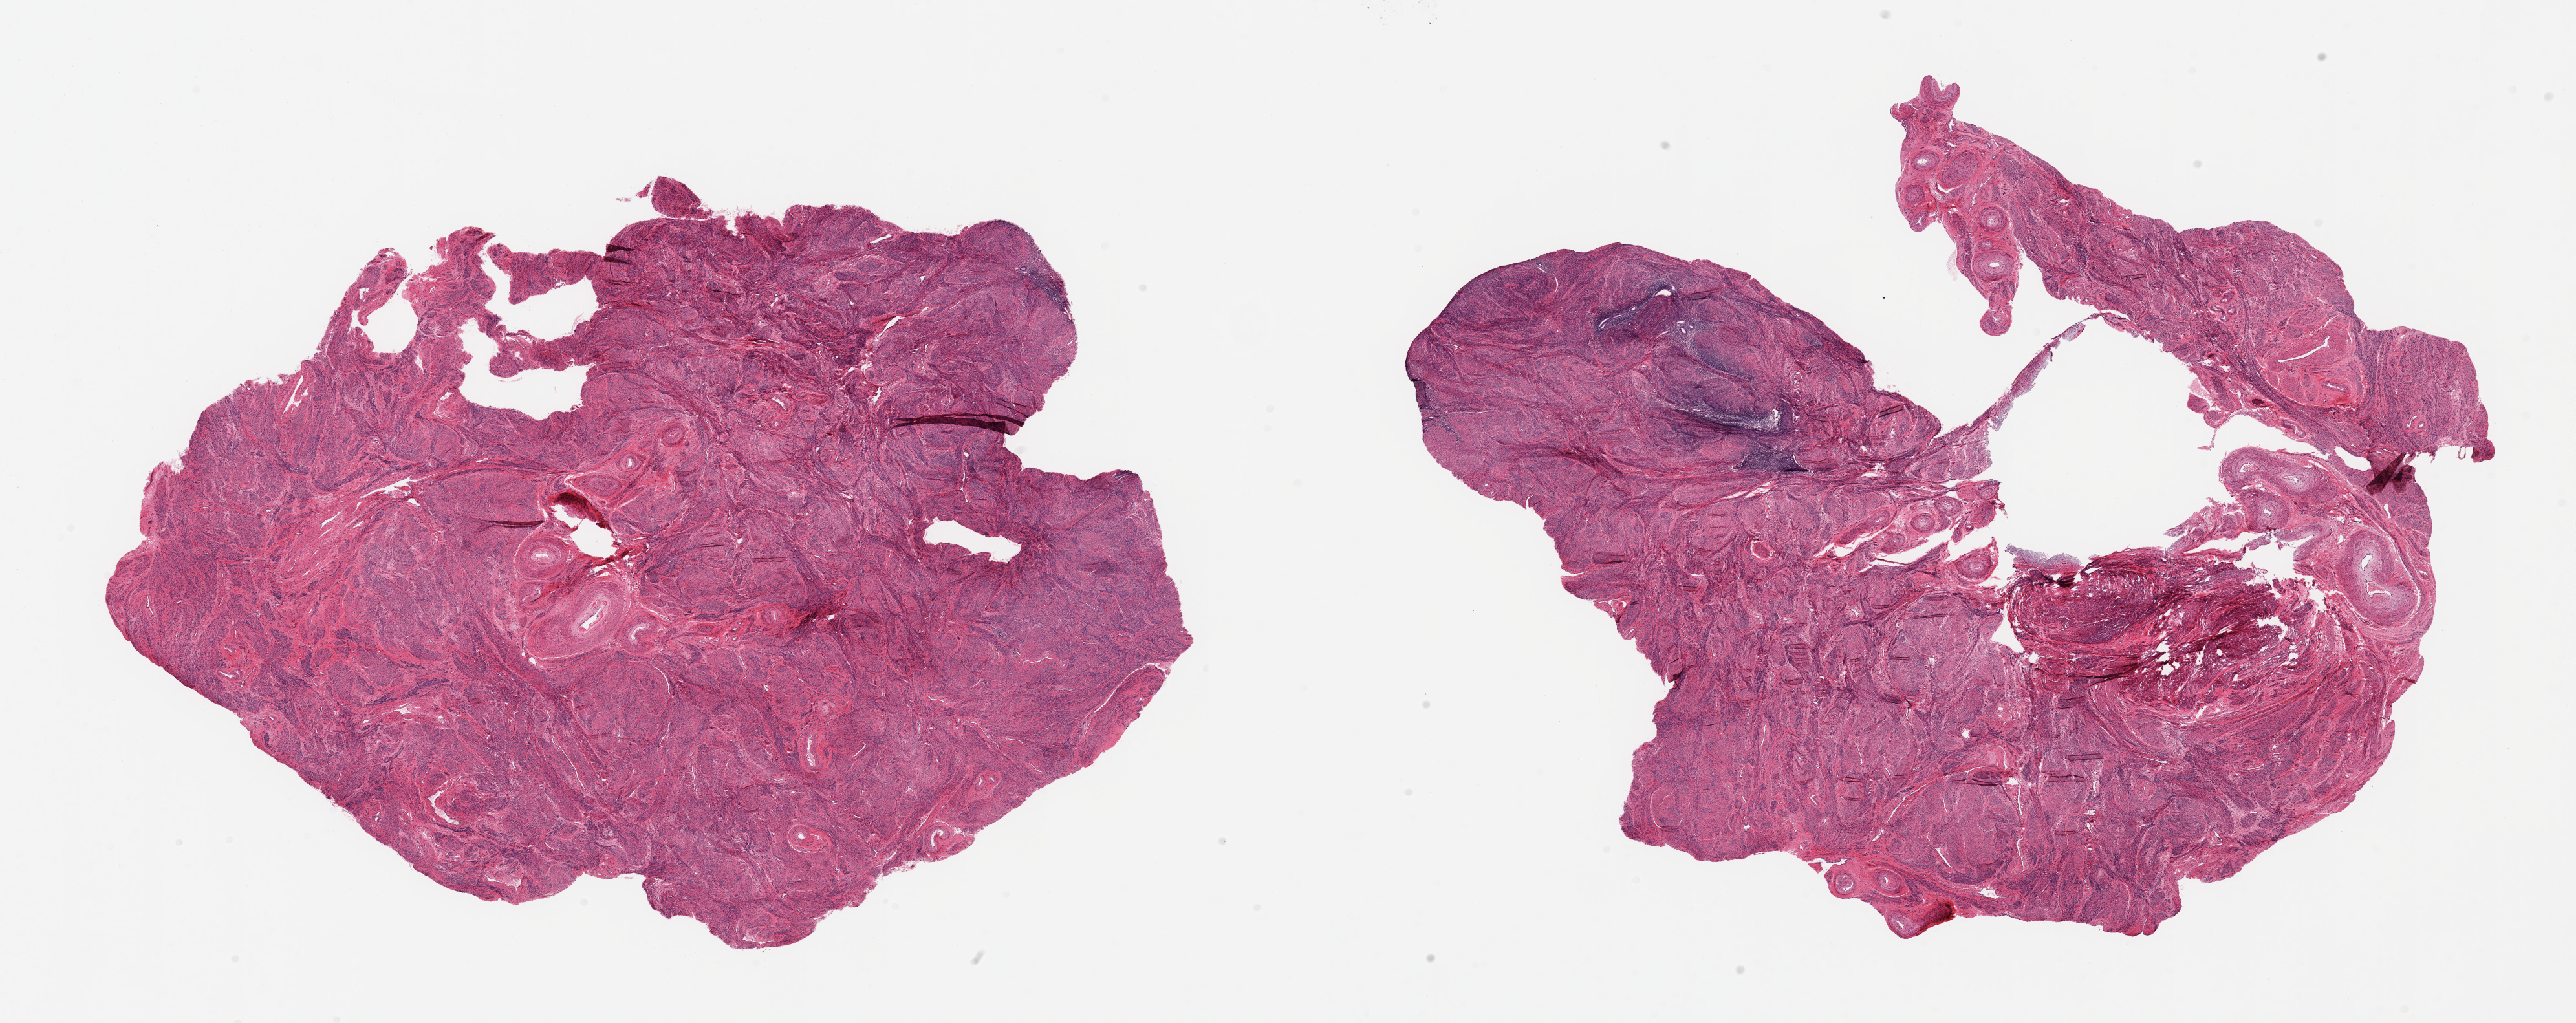
Whole-slide image, H&E stain — whole scanned area (about 31.5 x 12.5 mm, acquisition: 20x scan) shown as a low-resolution overview. PAXgene-fixed, paraffin-embedded tissue. Section of uterus (target tissue). Donor tissue sample. Donor: female.
Reviewer comment on this tissue sample: 2 pieces; mostly myometrium, small portion of endometrium in both.